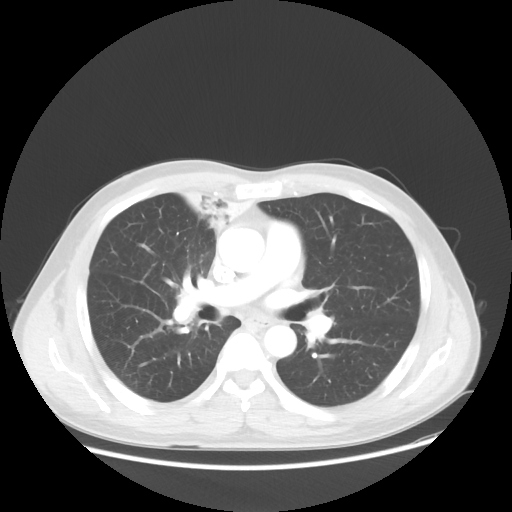
Chest CT, one axial slice. Position 30 of 56 along the scan axis. Reconstruction kernel STANDARD. Lung window (W 1500 / L -600 HU). 5 mm slice thickness. 512 × 512 image matrix, field of view 398 × 398 mm. Male patient, age 60 years. Case-level facts recorded for this patient, not image findings: clinical TNM (as recorded): T2a N1 M0.
Annotated regions visible in this slice (rectangle marked by the reading radiologist):
- lung tumour (recorded histology: squamous cell carcinoma): bounding box <179,182,266,253> (left, top, right, bottom; pixels)